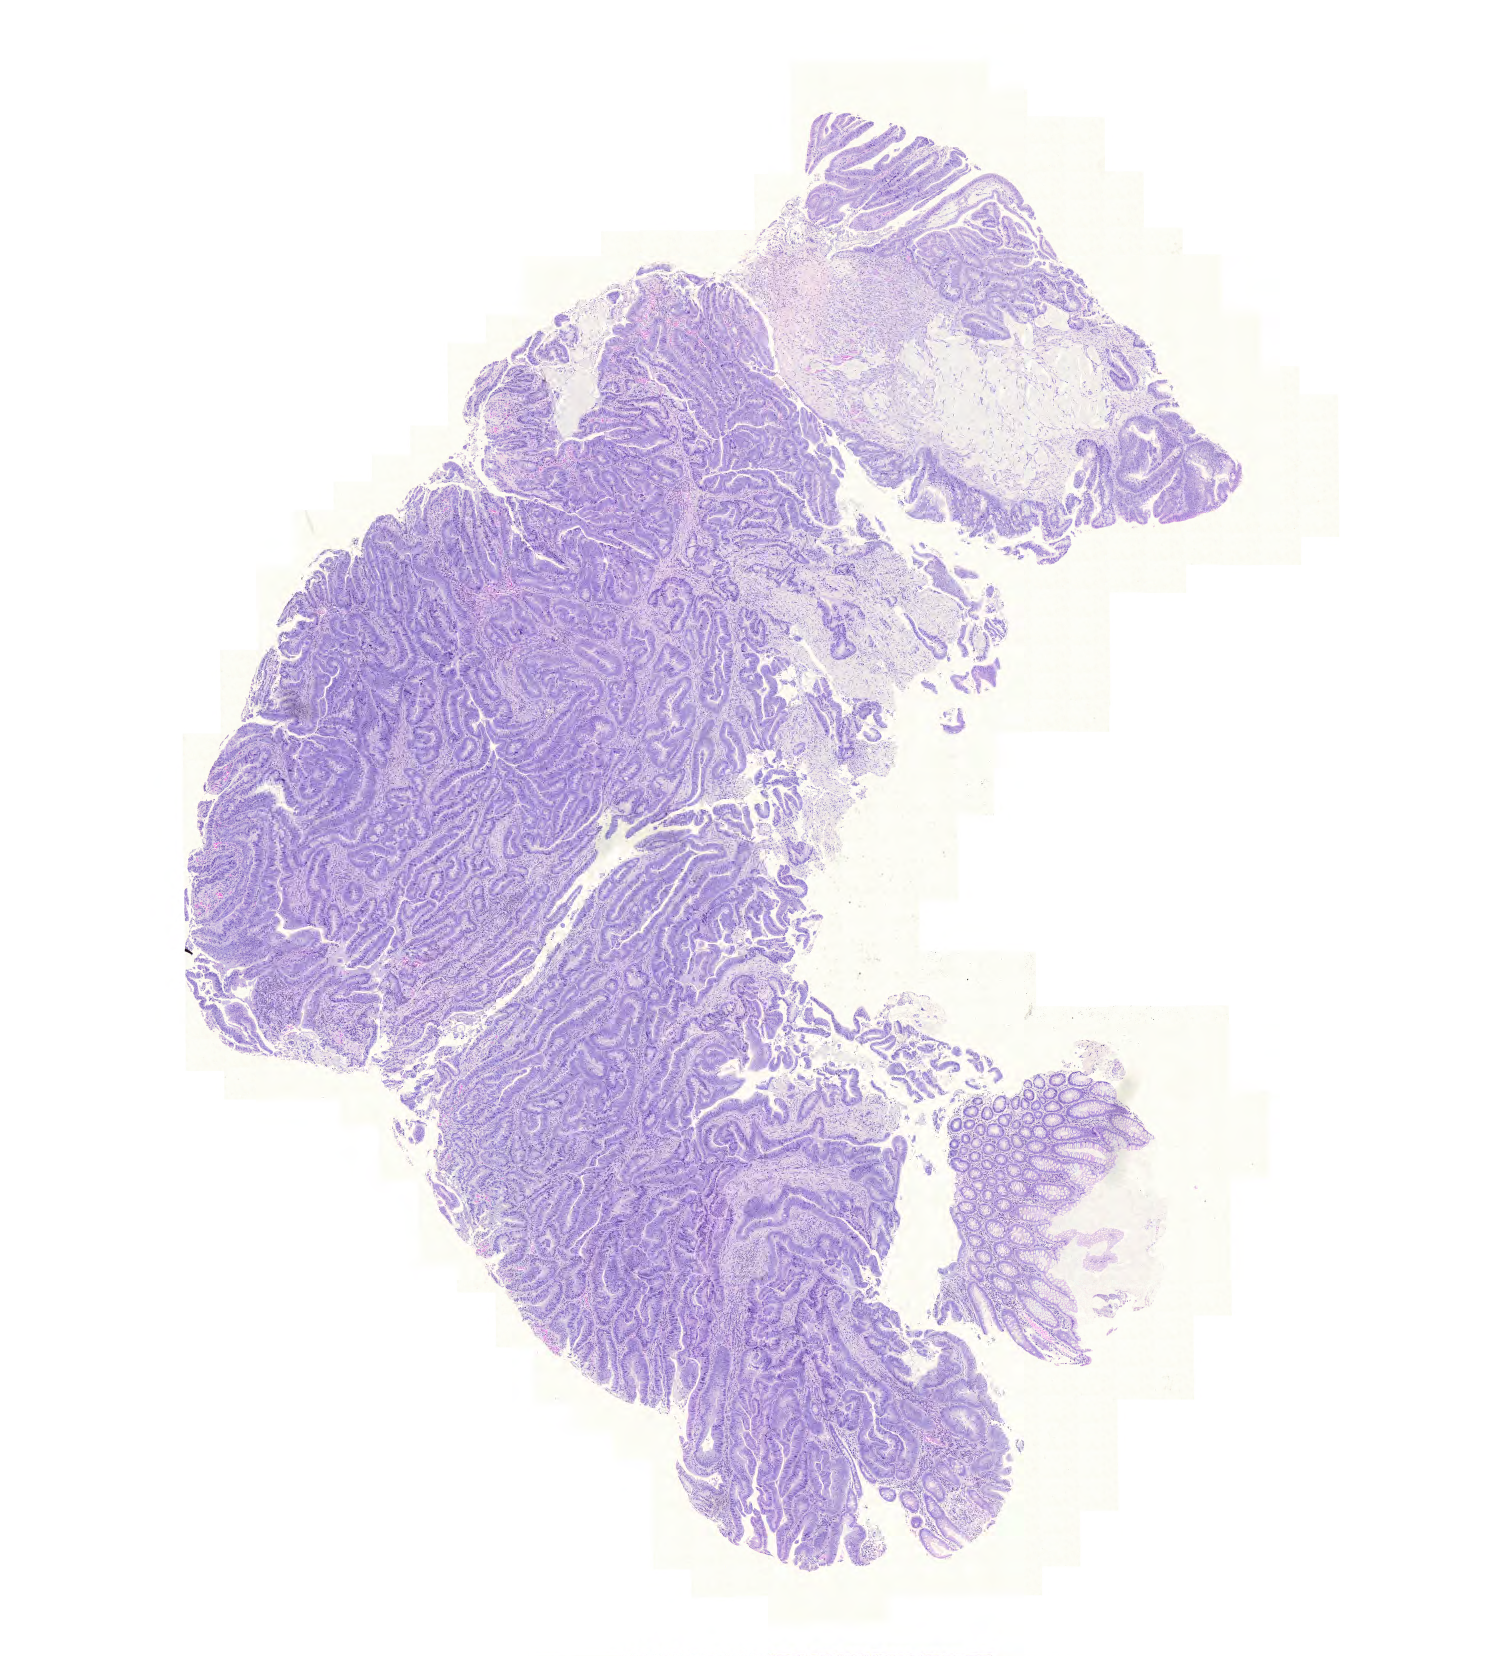
Digitized H&E-stained tissue section (whole slide), shown as a low-resolution overview of the whole scanned area (about 11.1 x 12.3 mm, from a 20x scan). FFPE section. Sample: primary tumour, colon. Patient: male, age at initial diagnosis 67 years.
Pathologic diagnosis: Mucinous adenocarcinoma. AJCC pathologic stage: IIA (6th edition). Lymph nodes positive (case pathology): 0 of 36 examined.